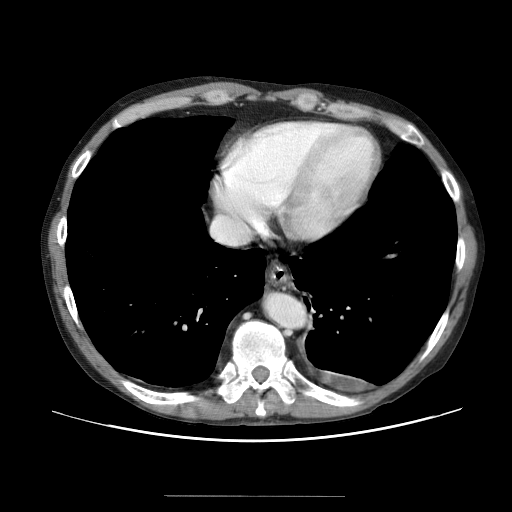
Contrast-enhanced abdominal CT (liver protocol), one axial slice. Slice 62 of 69 in the series (ordered by position). 120 kVp. Soft-tissue window (W 400 / L 40 HU). 2.5 mm slice thickness. 512 × 512 image matrix, field of view 380 × 380 mm. Case-level facts recorded for this patient, not image findings: diagnosis: hepatocellular carcinoma (patient treated with transarterial chemoembolisation; whether this scan precedes or follows treatment is not stated here); TNM stage (as recorded): Stage-IVB; Child-Pugh class: B; tumour differentiation: poorly differentiated; tumour nodularity: multinodular.
Annotated regions visible in this slice (semi-automatically segmented with operator editing):
- liver parenchyma outside the tumour (the mass and vessels are separate outlines, so this box may not span the whole liver): box from (x=122, y=193) to (x=152, y=220) px